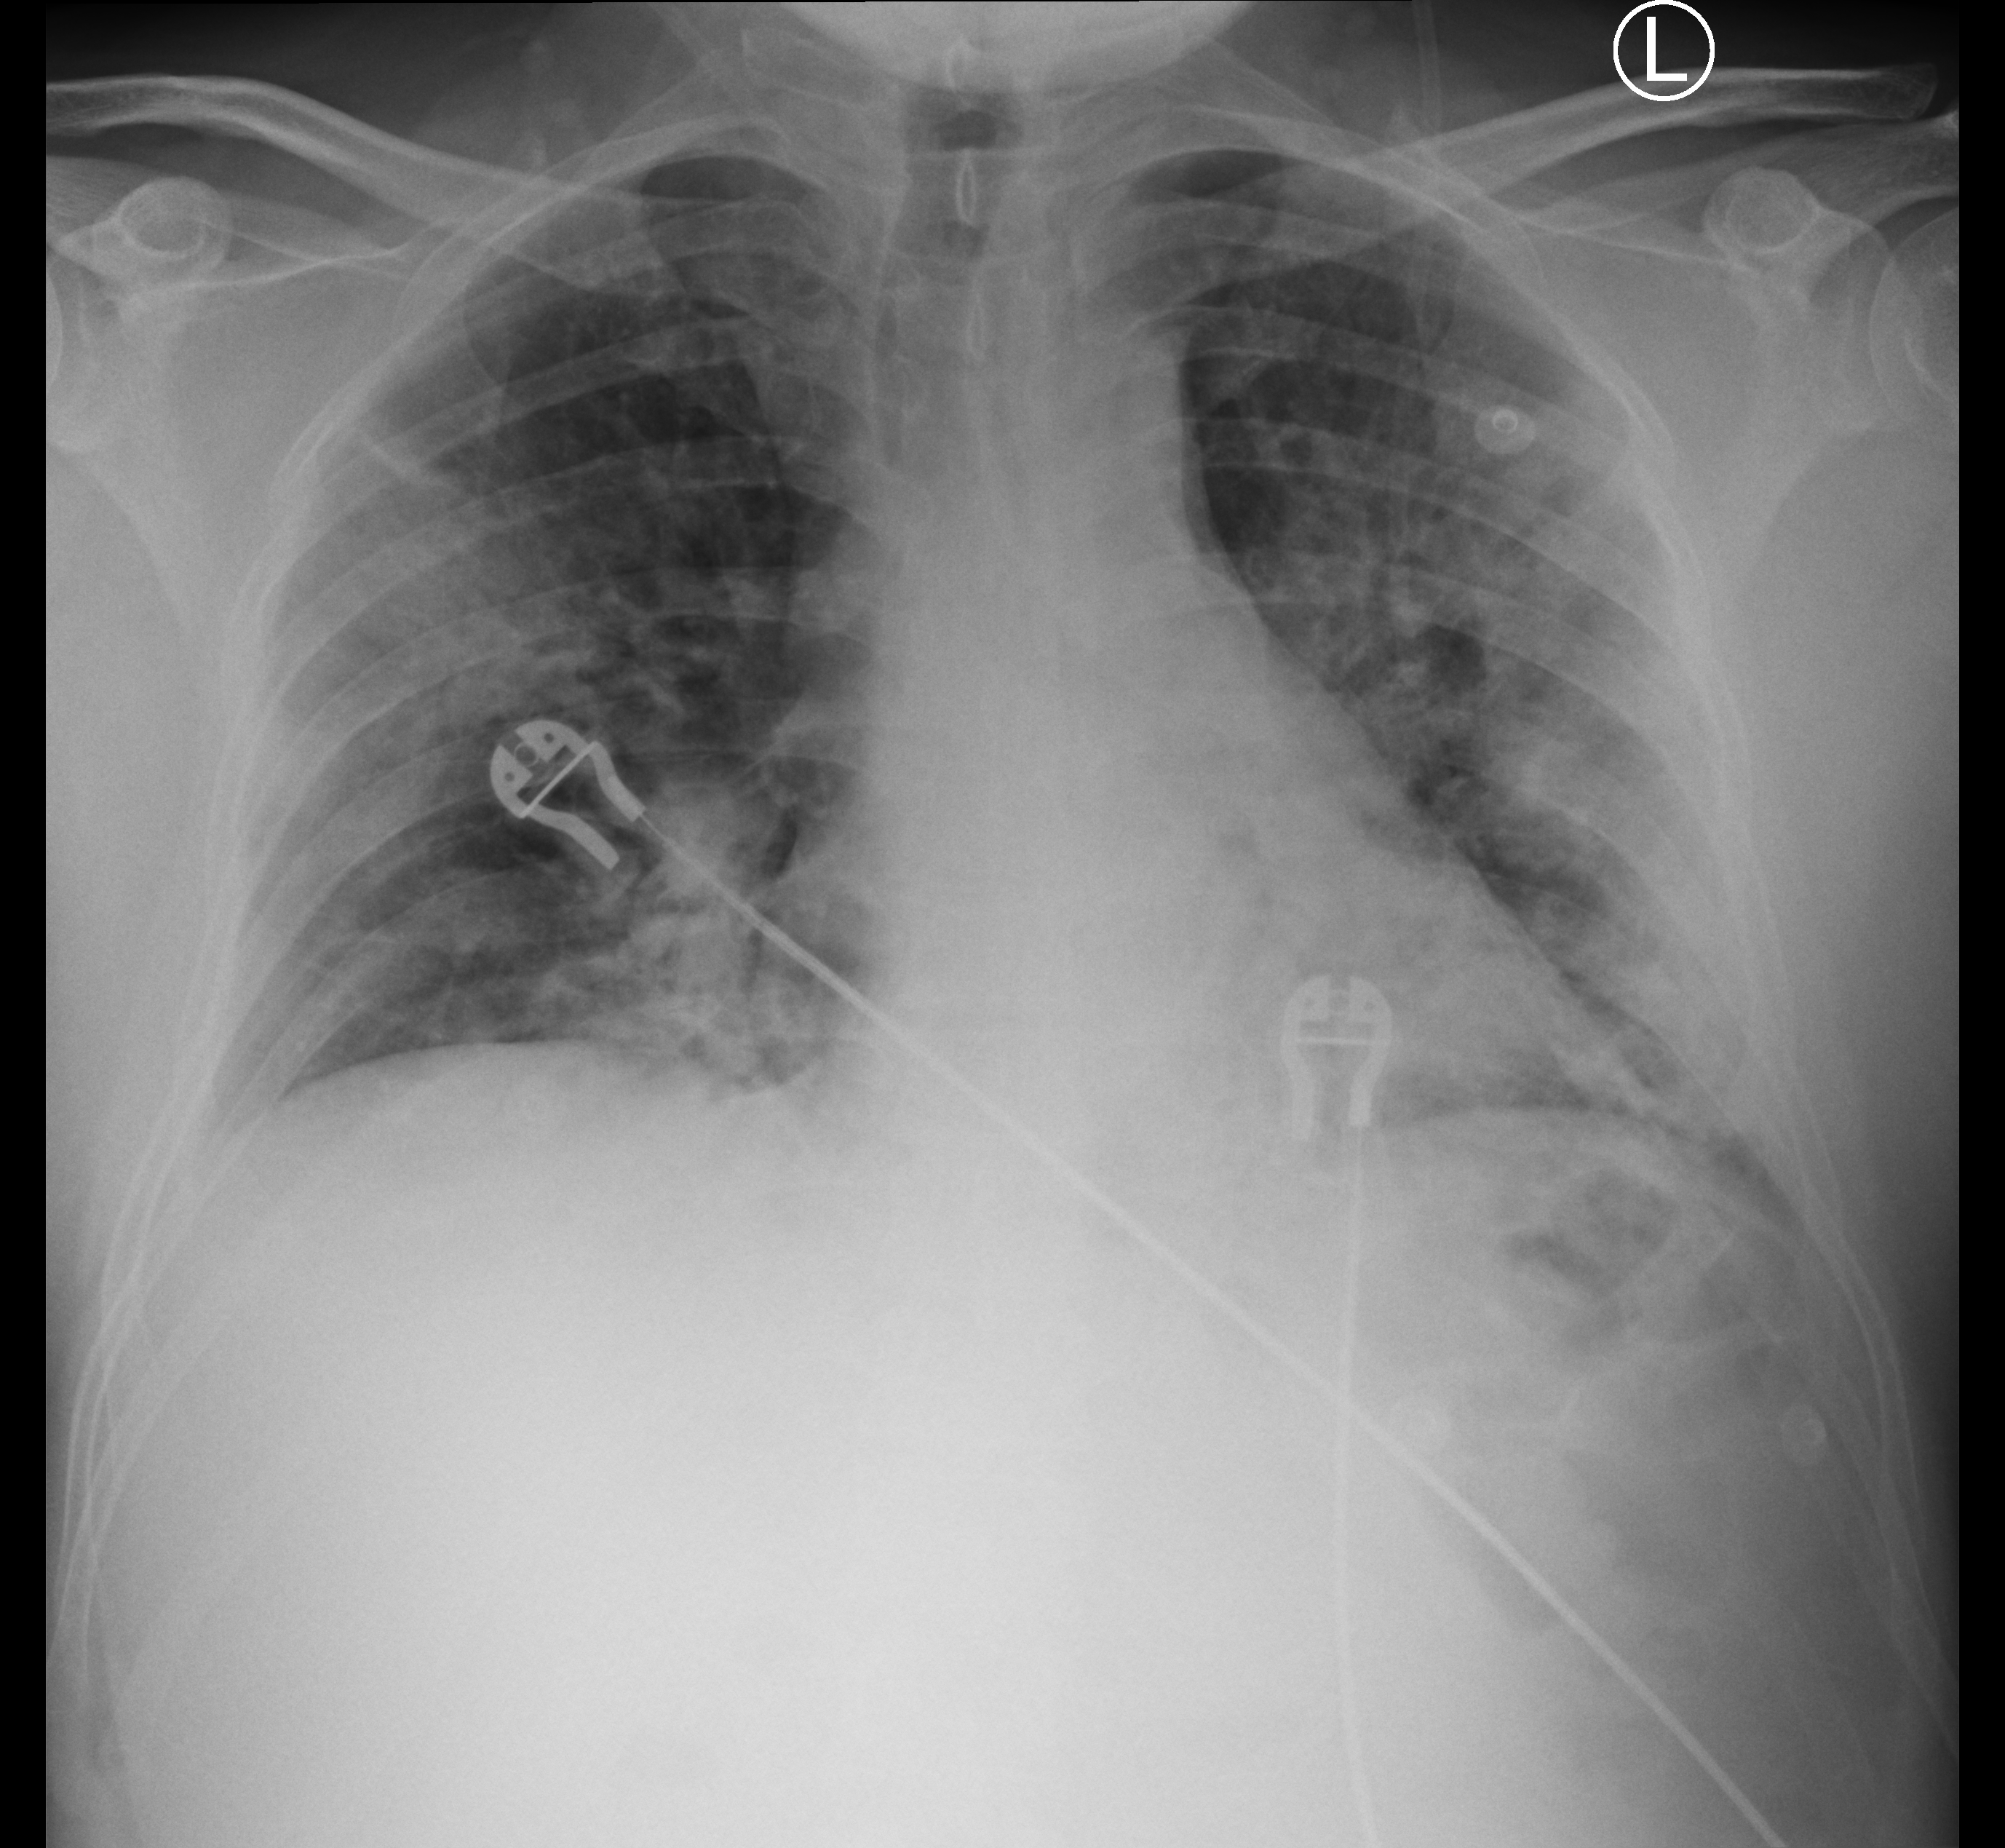
Chest X-ray (portable); anteroposterior (AP) projection. Male patient hospitalised with COVID-19, age 18–59 years.
Admission-level facts for this patient (not findings on this image; timing relative to this image not recorded): chronic kidney disease (admission record): no; length of hospital stay: 9 days; mechanically ventilated during this hospital stay: no.